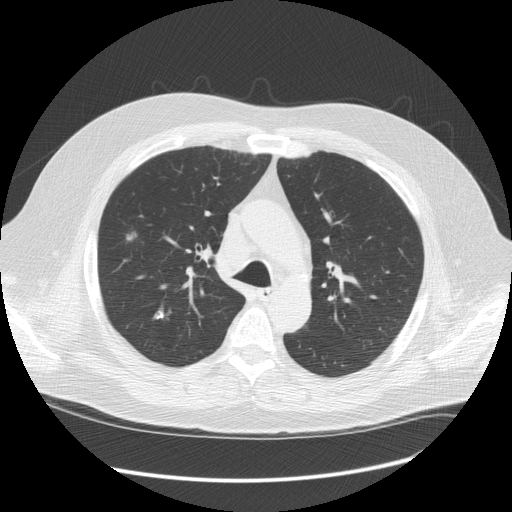
Low-dose screening chest CT, one axial slice. Position 90 of 128 along the scan axis. Reconstruction kernel STANDARD. 120 kVp. Lung window (W 1500 / L -600 HU). 2.5 mm slice thickness. 512 × 512 image matrix.
Structures marked on this image (expert manual segmentation):
- lesion 1 (tumor, upper lobe of right lung): bounding box (x1, y1, x2, y2) in pixels: (126, 232, 137, 241)